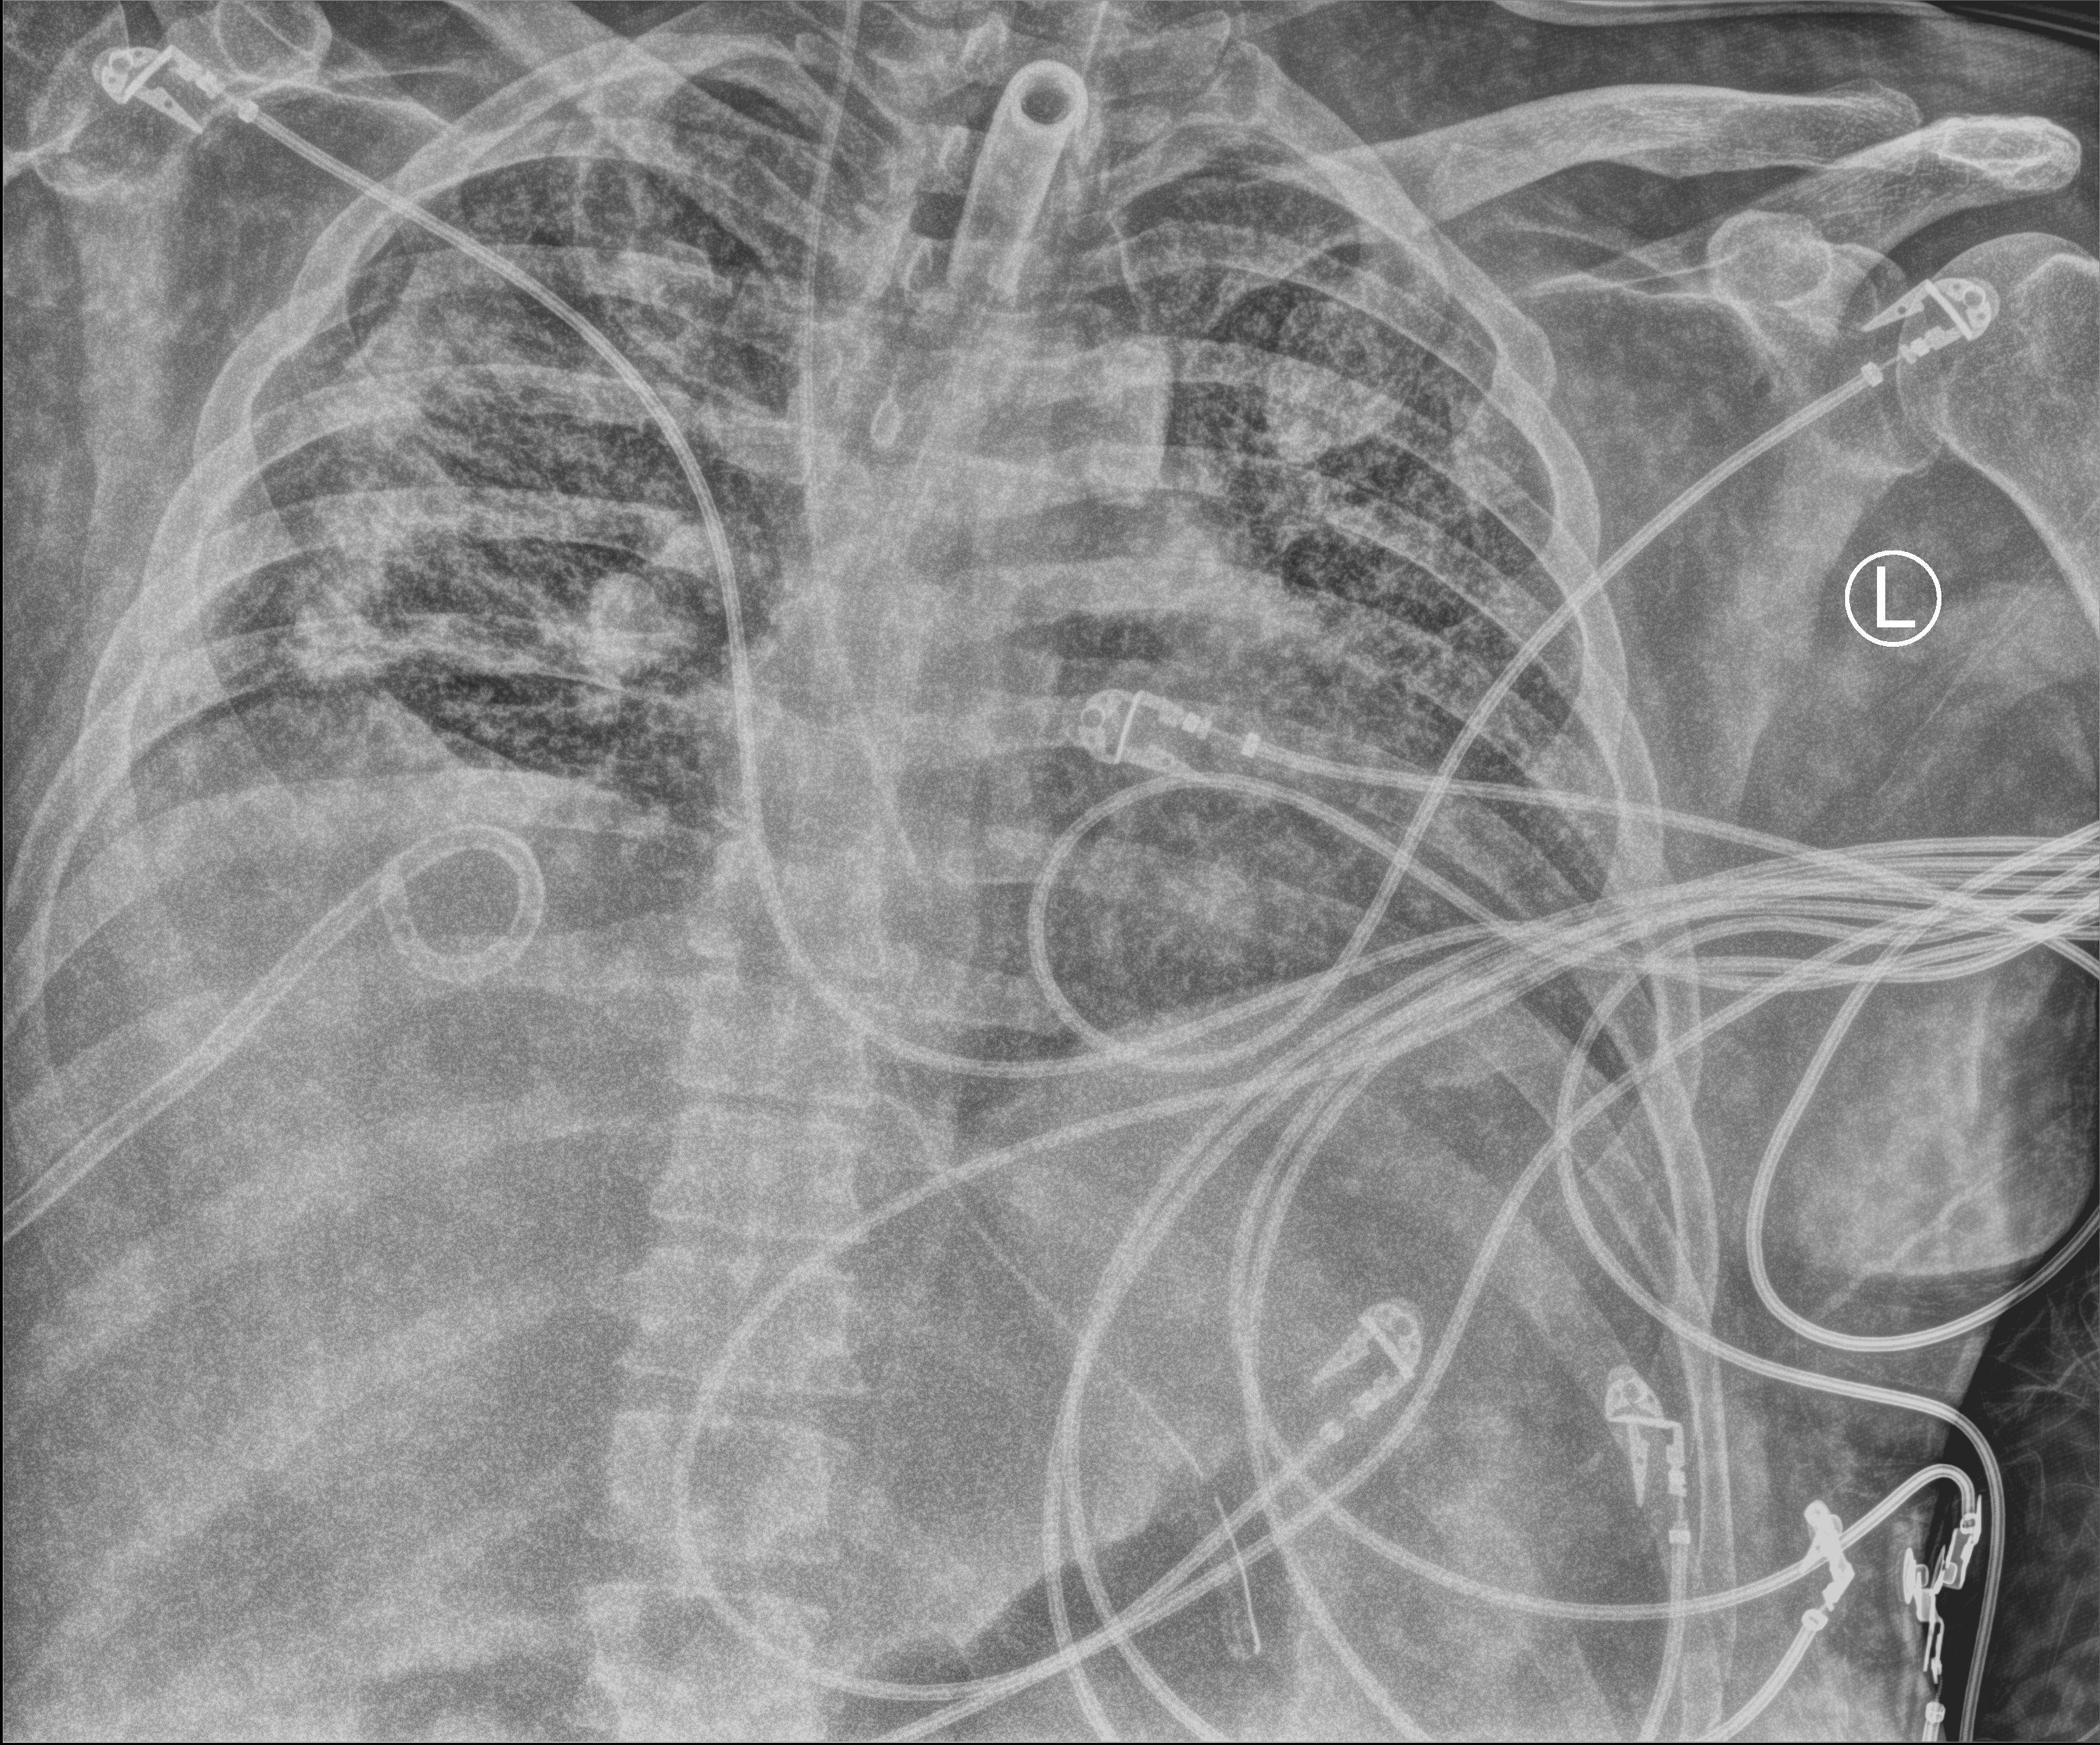
Chest X-ray (portable), anteroposterior (AP) projection. Male patient hospitalised with COVID-19, age 18–59 years.
From the hospital-stay record, not from the radiograph (when in the stay this image was taken is not recorded): admitted to intensive care during this hospital stay: yes; mechanically ventilated during this hospital stay: yes; length of hospital stay: 80 days.